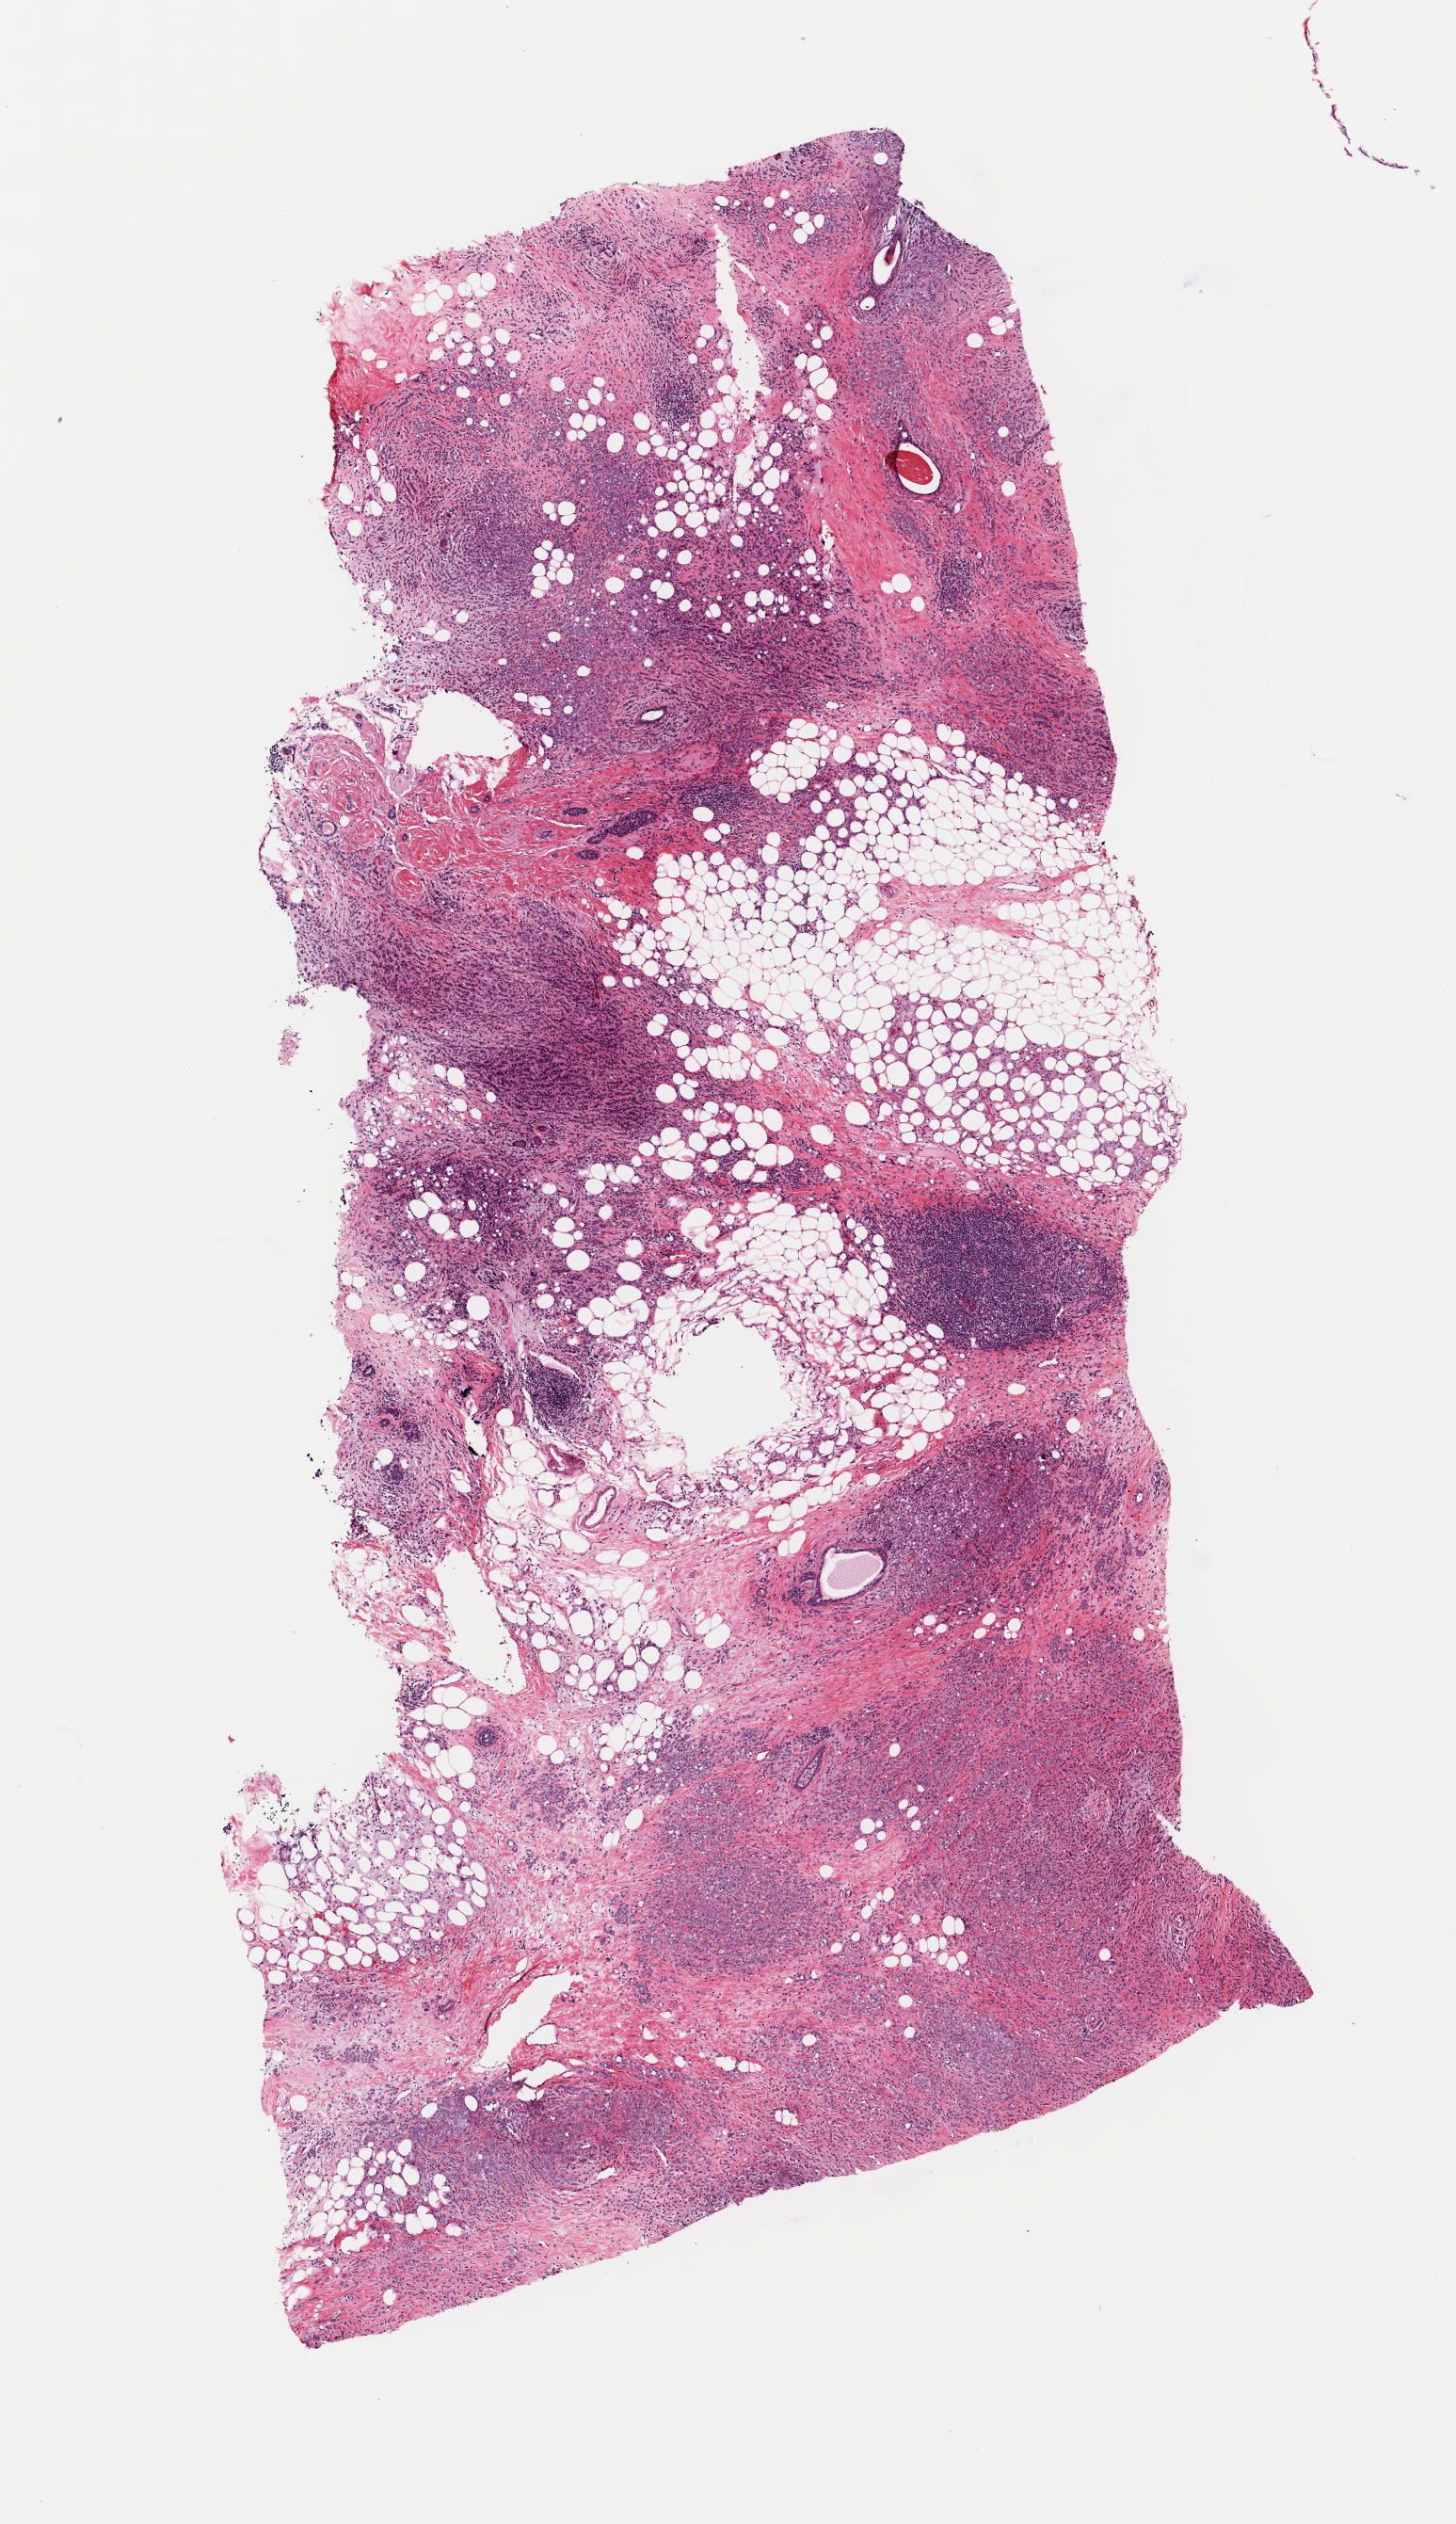
Hematoxylin and eosin (H&E) stained whole-slide image, shown as a low-resolution overview of the whole scanned area (about 6.1 x 10.6 mm), frozen section, sample: primary tumour, breast. Female, age 68 years at initial diagnosis. Pathologist review of this section (percent, as recorded): tumour cells 60%, tumour nuclei 70%, normal cells 5%, stromal cells 35%, necrosis 0%. Infiltration values recorded for this section: lymphocyte infiltration 0%, monocyte infiltration 0%, neutrophil infiltration 0%.
Laterality: left. AJCC pathologic stage: IIB. Diagnosis: Lobular carcinoma, NOS.